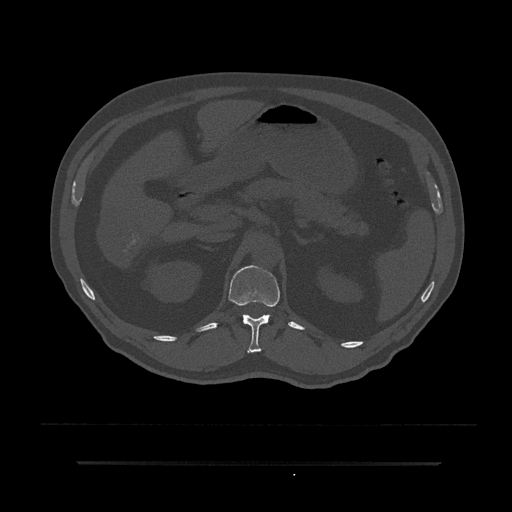
CT including the spine, one axial slice; position 198 of 797 along the scan axis; 120 kVp; bone window (W 1800 / L 400 HU); 0.5 mm slice thickness; 512 × 512 image matrix, field of view 464 × 464 mm. Patient: male, 59 years. From the clinical record (not read from this slice): primary cancer: bile ducts; vertebrae with lytic lesions (as recorded): T10.
Outlined on this slice (semi-automatically segmented with operator editing):
- T12 vertebra: bounding box [x1, y1, x2, y2] px = [229, 266, 280, 354]